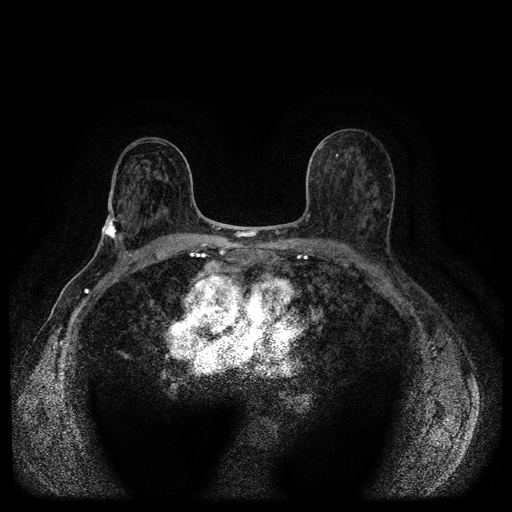
Breast MRI (dynamic contrast-enhanced, multi-phase), one axial slice; slice 61 of 116 in the series (ordered by position); dynamic contrast-enhanced series, time point 2 of 5 at this slice position (early post-contrast); 1.5 T; TE 2.7 ms, TR 5.4 ms; 2 mm slice thickness; 512 × 512 image matrix, field of view 340 × 340 mm. Patient: female, 75 years.
Structures marked on this image (semi-automatically segmented with operator editing):
- breast lesion (labelled 'tumour' in the annotation; benign lesions carry a separate 'benign' label): box from (x=101, y=214) to (x=119, y=242) px